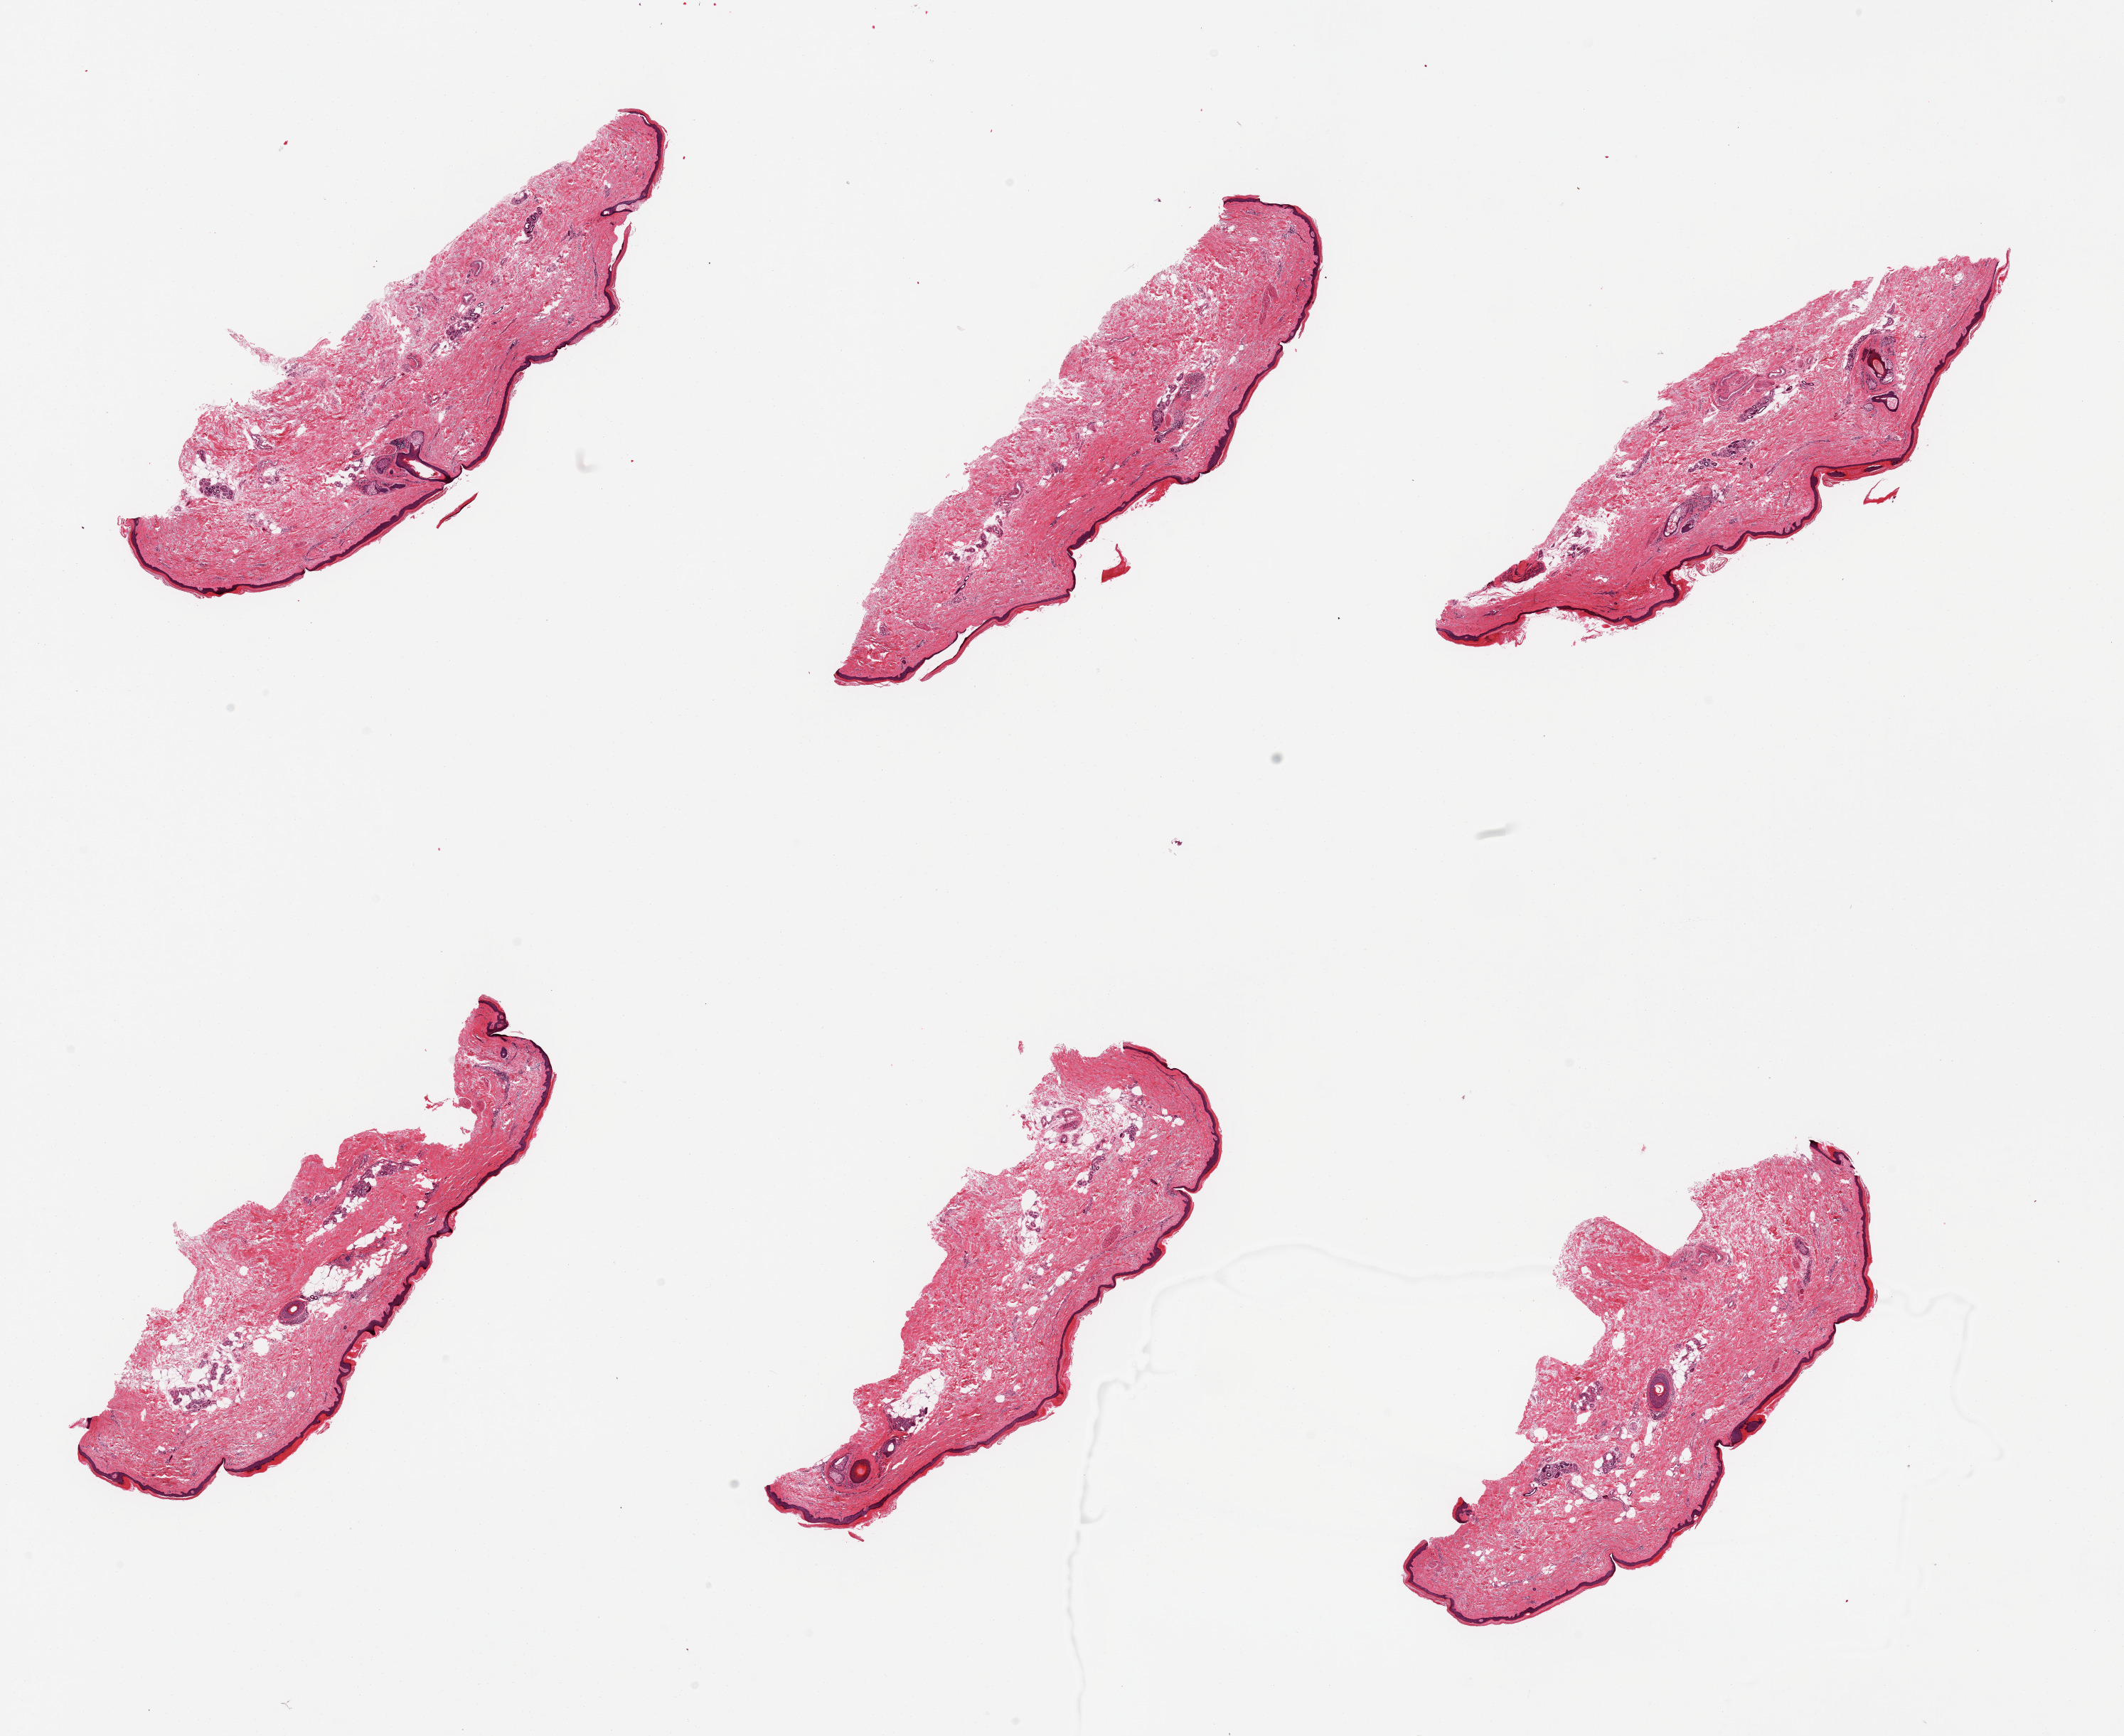
Digitized hematoxylin and eosin (H&E)-stained section — shown as a low-resolution overview of the whole scanned area (about 23.6 x 19.3 mm, slide scanned at 20x). PAXgene-fixed paraffin-embedded (PFPE) section. Section of skin of lower leg (target tissue). Donor tissue sample. Male donor.
• pathologist's review note for this sample: 6 pieces; small amount of internal fat, epidermis measures 35 microns